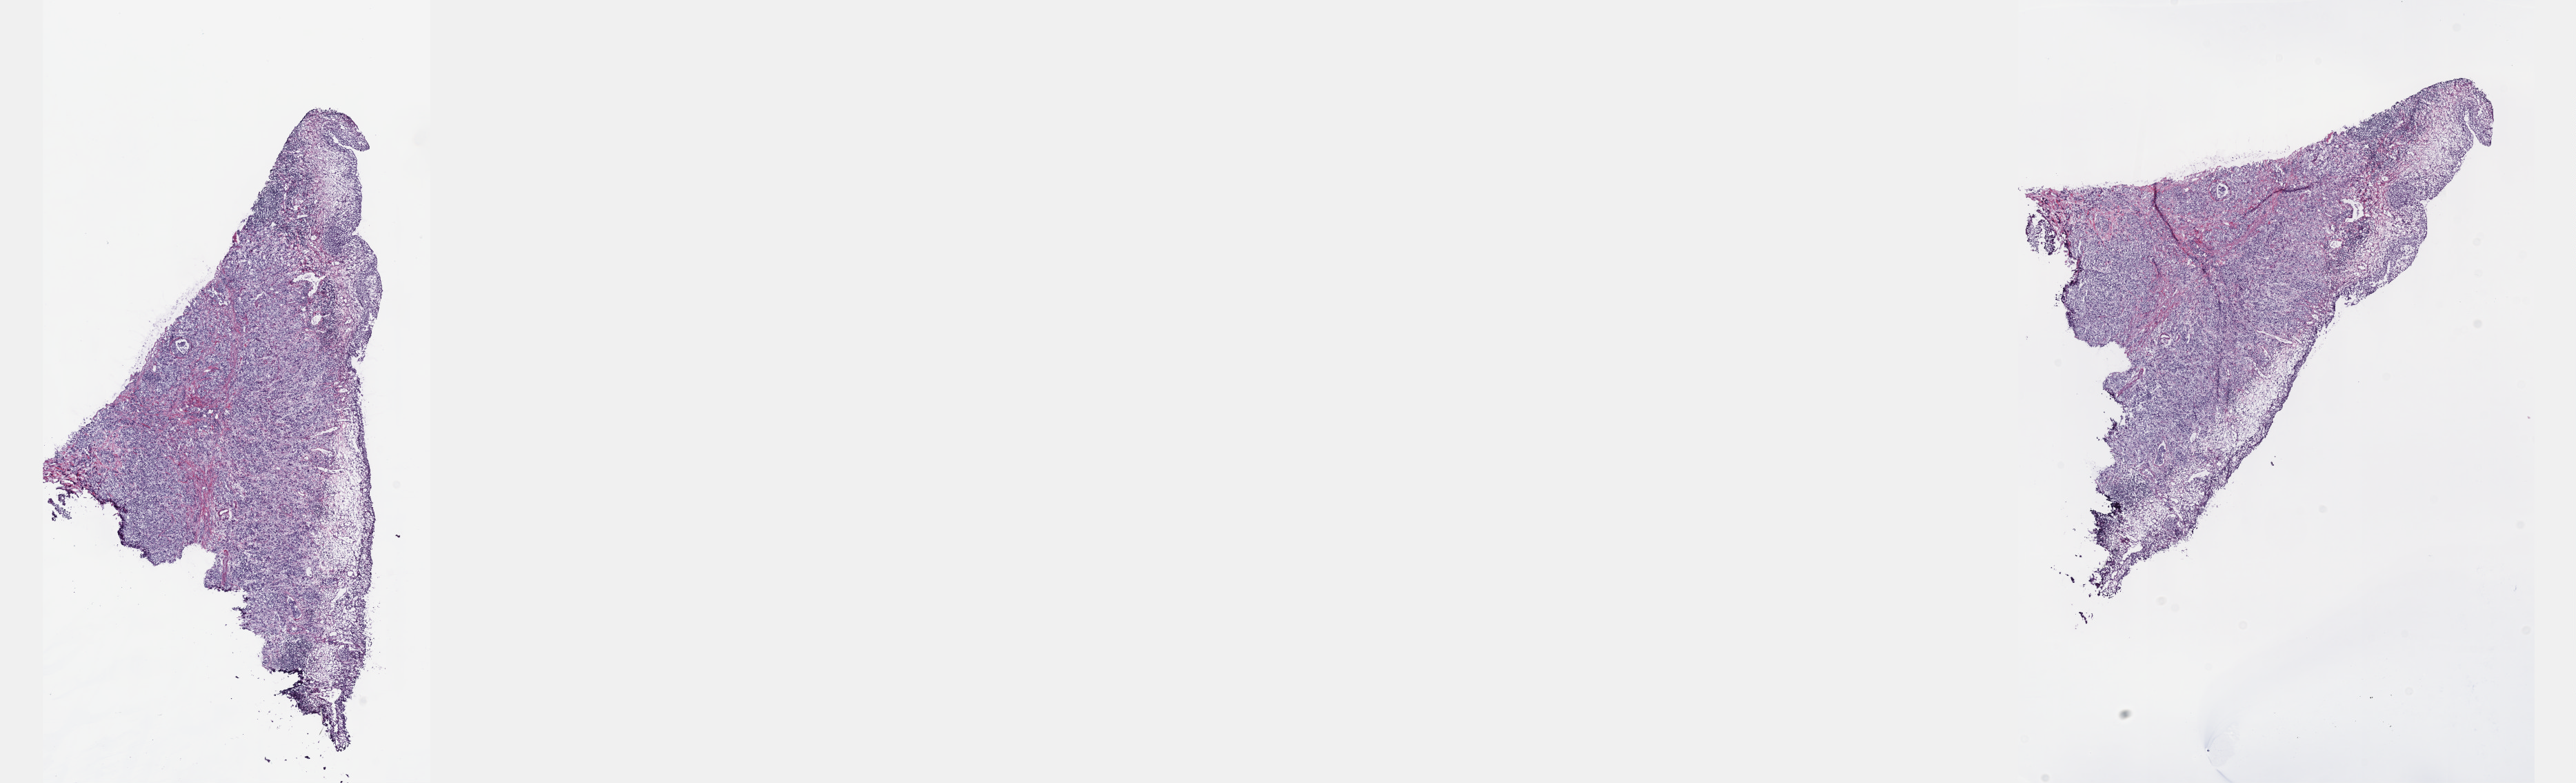
Hematoxylin and eosin (H&E) stained whole-slide image — whole scanned area (about 30.2 x 9.2 mm, slide scanned at 40x) shown as a low-resolution overview, frozen section from the top of the tissue portion, primary tumour sample from the bladder. Female patient; age at initial diagnosis 60 years.
Diagnosis: Transitional cell carcinoma.